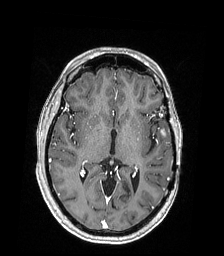
Brain MRI from a brain-tumour surgery series, one axial slice; slice 103 of 168 in the series (ordered by position); T1-weighted post-contrast; 1 mm slice thickness; 224 × 256 image matrix, field of view 224 × 256 mm. From the clinical record (not read from this slice): histopathology: Astrocytoma; WHO grade: 4; IDH mutation: yes; tumour location: Left Temporal.
Structures marked on this image (manually delineated by an expert):
- tumour: bounding box (x1, y1, x2, y2) in pixels: (161, 130, 166, 136)